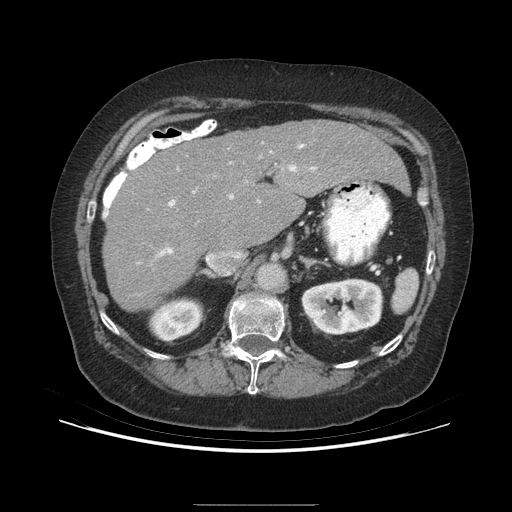
Contrast-enhanced abdominal CT (liver protocol), one axial slice. Position 156 of 192 along the scan axis. Reconstruction kernel STANDARD. 140 kVp. Soft-tissue window (W 400 / L 40 HU). 2.5 mm slice thickness. 512 × 512 image matrix, field of view 400 × 400 mm. Case-level facts recorded for this patient, not image findings: diagnosis: hepatocellular carcinoma (patient treated with transarterial chemoembolisation; whether this scan precedes or follows treatment is not stated here); TNM stage (as recorded): Stage-I; Child-Pugh class: A; tumour differentiation: moderately differentiated; tumour nodularity: uninodular.
Annotated regions visible in this slice (semi-automatically segmented with operator editing):
- liver parenchyma outside the tumour (the mass and vessels are separate outlines, so this box may not span the whole liver): bounding box [x1, y1, x2, y2] px = [102, 120, 408, 312]
- liver vessels: [158, 144, 316, 256]